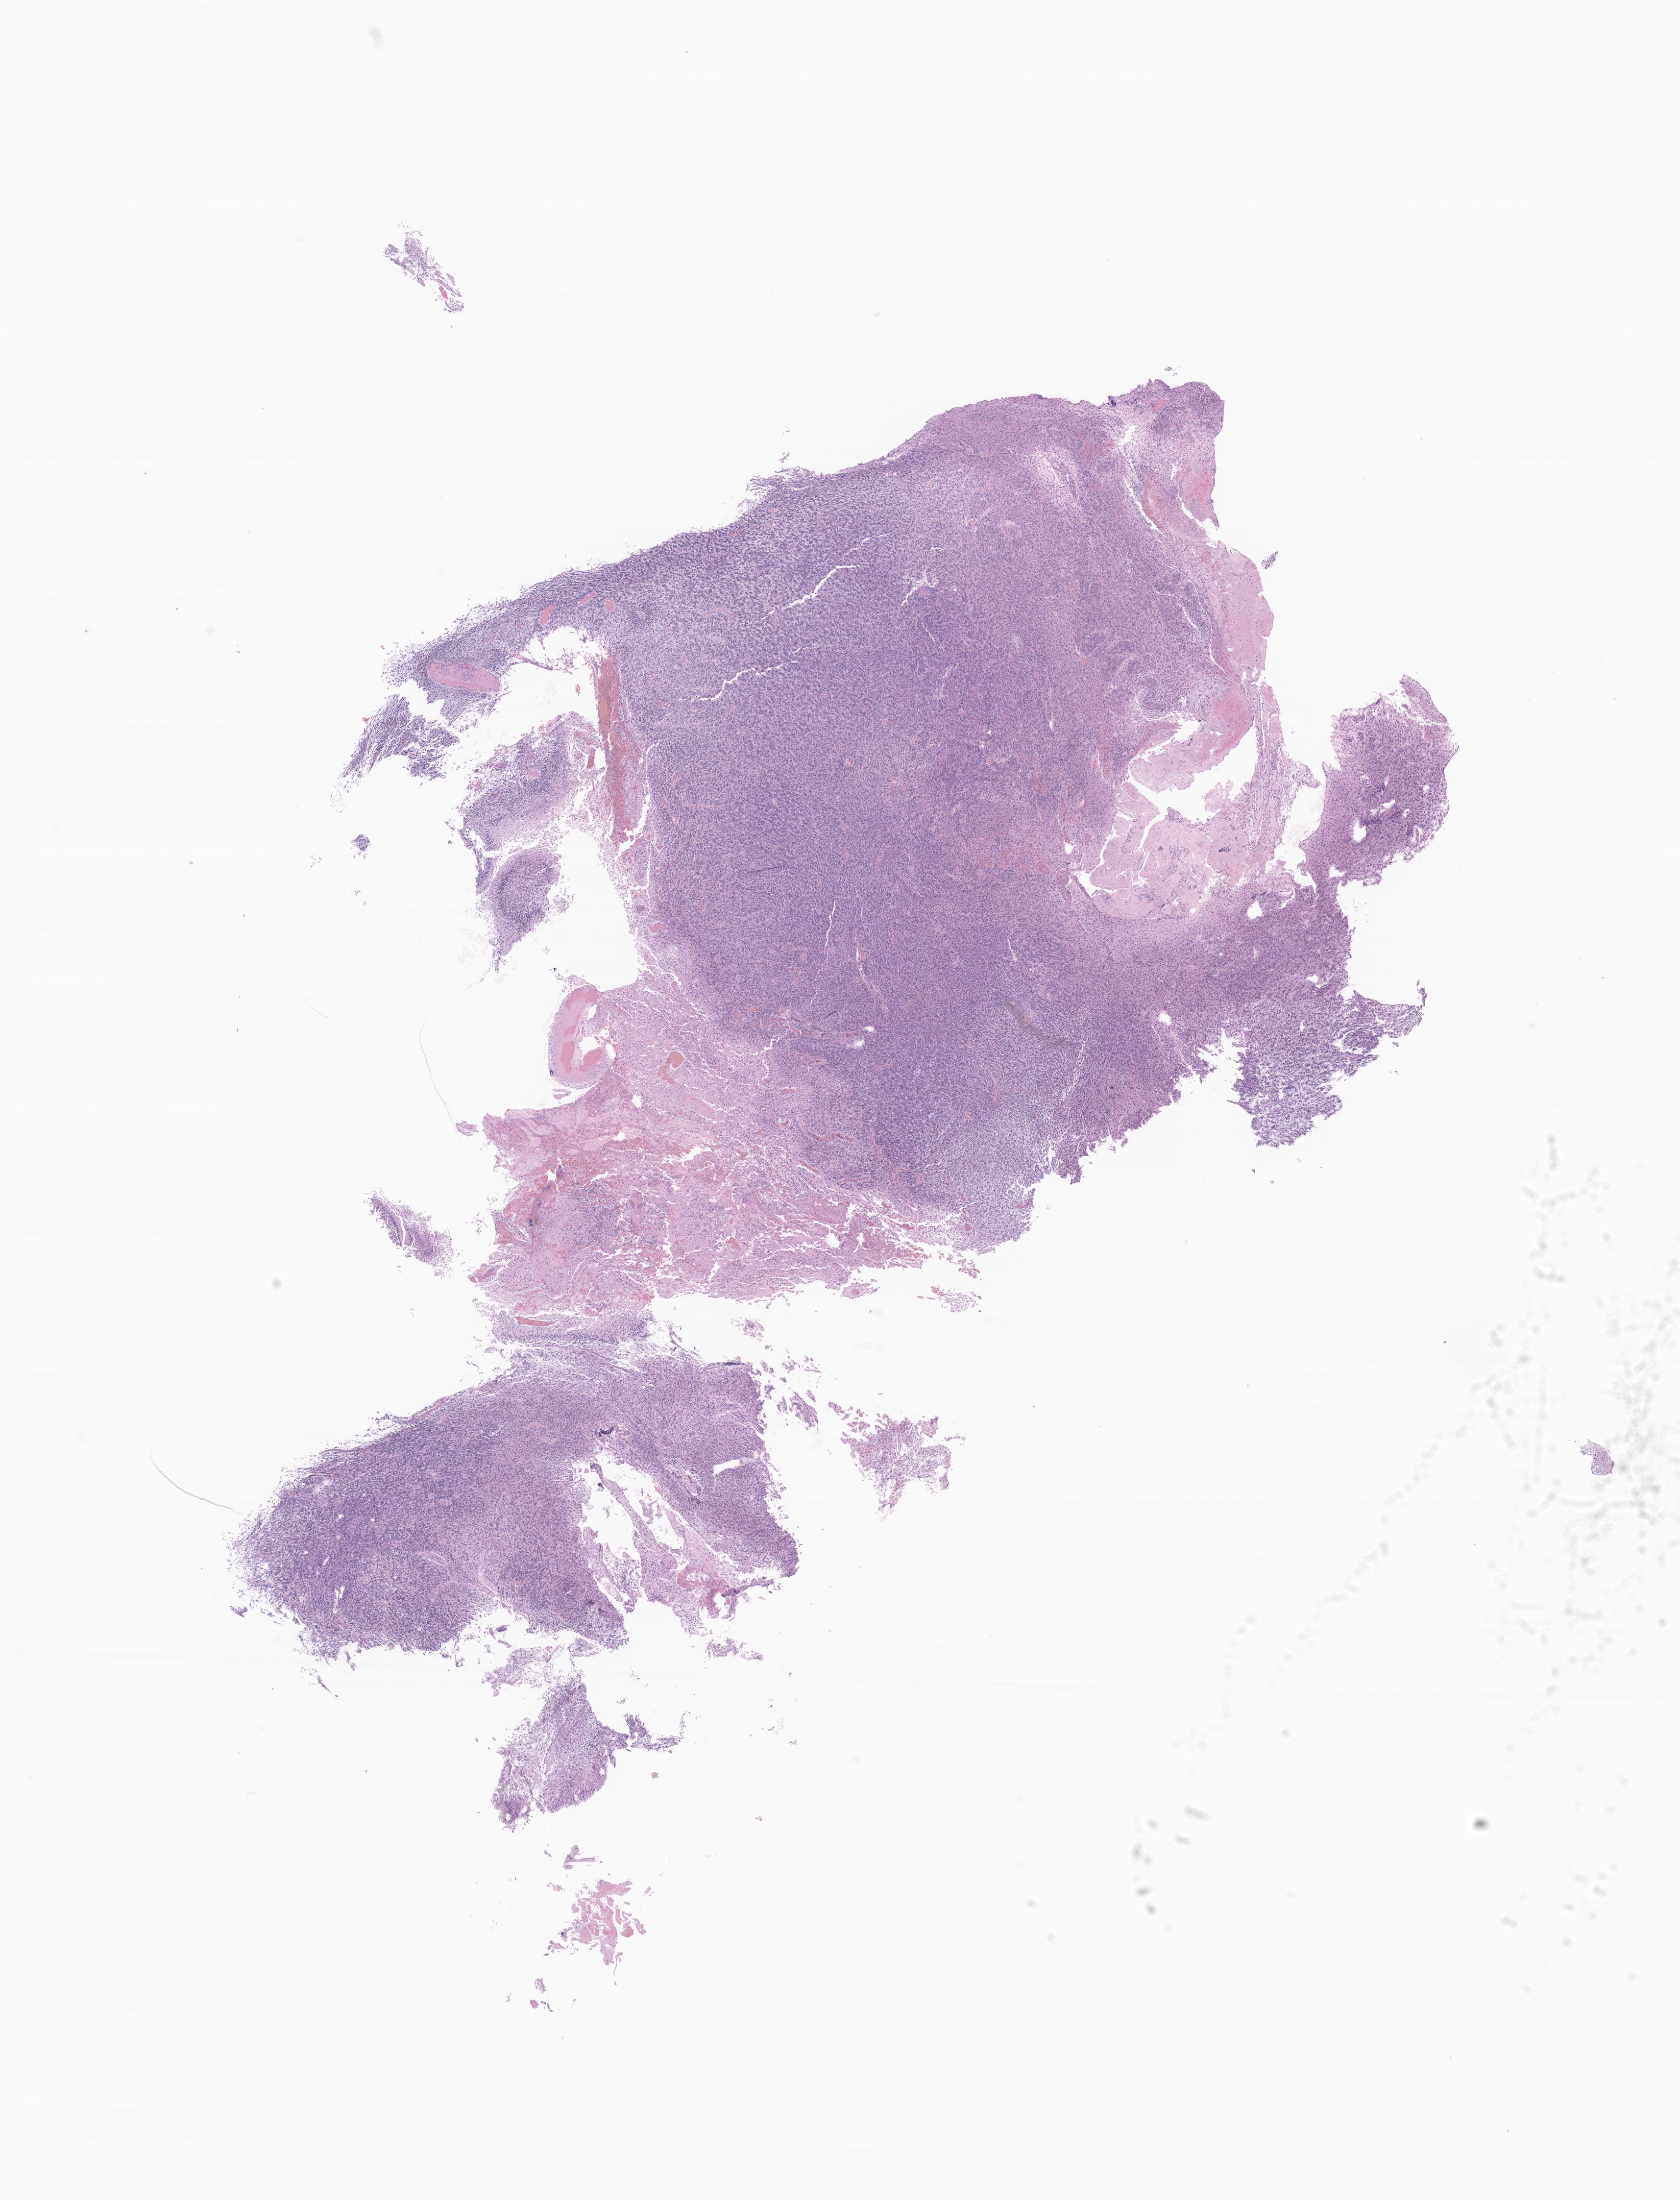
Digitized H&E-stained section of tumor tissue from the spinal cord, whole scanned area (about 13.9 x 18.2 mm) shown as a low-resolution overview; FFPE section. Male patient, age 149 months (12 years 5 months).
Diagnosis (ICD-O-3 morphology term): Glioma, malignant.